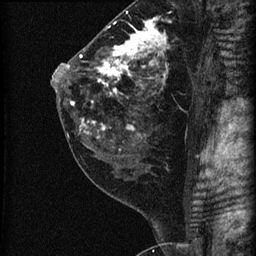
Breast MRI (dynamic contrast-enhanced), one sagittal slice. Slice 35 of 60 in the series (ordered by position). Dynamic contrast-enhanced series, image 2 of 3 at this slice position (ordered by acquisition). 1.5 T. TE 4.2 ms, TR 22.7 ms. 1.8 mm slice thickness. 256 × 256 image matrix. Patient: female, 45 years. Case-level facts recorded for this patient, not image findings: setting: breast cancer imaged before/during neoadjuvant chemotherapy; receptor status: HR-positive, HER2-negative.
Outlined on this slice (semi-automatically segmented with operator editing):
- analysis volume of interest (the breast-tissue region the enhancement analysis was run in; not a lesion): bounding box [x1, y1, x2, y2] px = [74, 11, 205, 140]
- tumour enhancement mask (voxels above the 90 % enhancement threshold inside the analysis volume of interest): [79, 18, 167, 133]